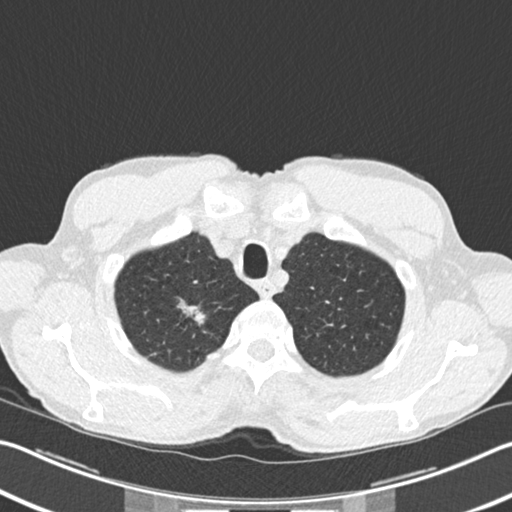
Low-dose screening chest CT, one axial slice; slice 193 of 220 in the series (ordered by position); reconstruction kernel B30f; 120 kVp; lung window (W 1500 / L -600 HU); 2 mm slice thickness; 512 × 512 image matrix, field of view 342 × 342 mm.
Annotated regions visible in this slice (expert manual segmentation):
- lesion 1 (tumor, upper lobe of right lung): bounding box (x1, y1, x2, y2) in pixels: (179, 300, 205, 325)